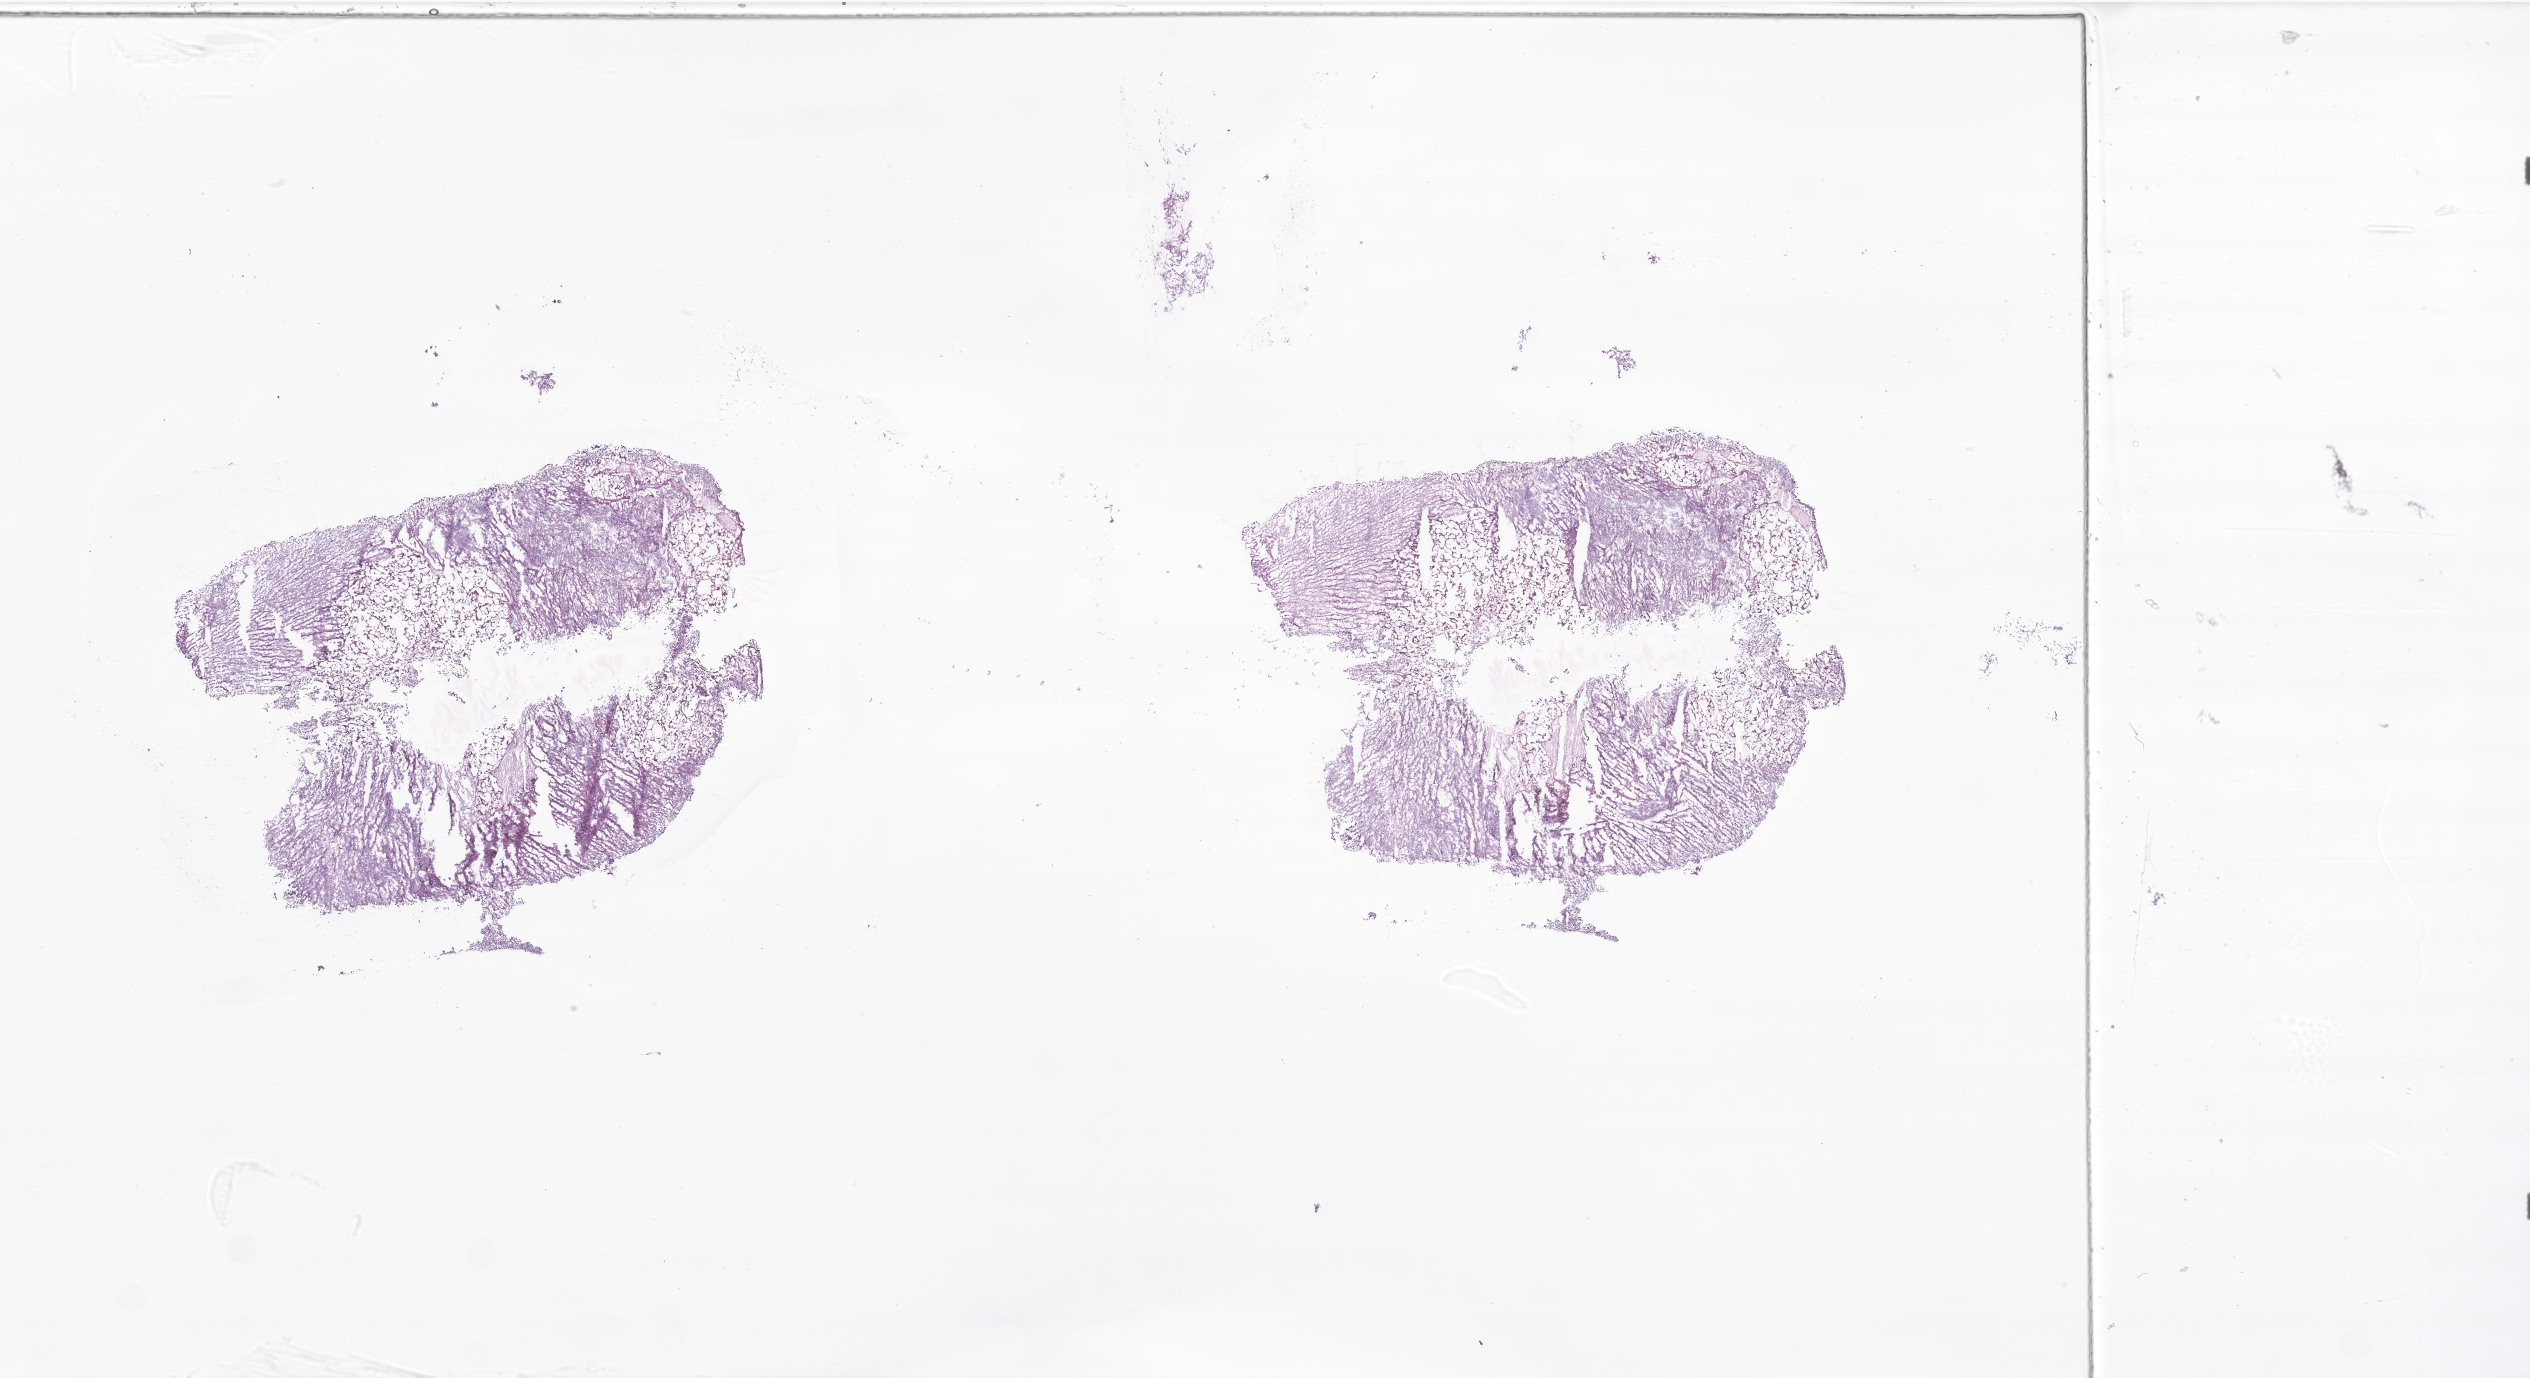
Digitized hematoxylin and eosin (H&E)-stained section of tumor tissue from the brain — low-resolution overview of the scanned area, about 42.7 x 23.2 mm, frozen section. Male patient, age 34 months (2 years 10 months).
Diagnosis: Neoplasm, malignant.